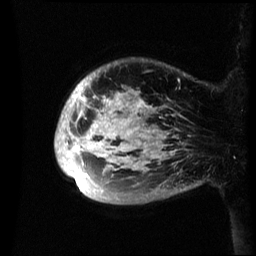
Breast MRI (dynamic contrast-enhanced), one sagittal slice. Slice 7 of 60 in the series (ordered by position). Dynamic contrast-enhanced series, image 2 of 3 at this slice position (ordered by acquisition). 1.5 T. TE 4.2 ms, TR 8.4 ms. 2.4 mm slice thickness. 256 × 256 image matrix. Female patient, age 48 years.
Structures marked on this image (semi-automatic segmentation, software-assisted and operator-edited):
- analysis volume of interest (the breast-tissue region the enhancement analysis was run in; not a lesion): bounding box (x1, y1, x2, y2) in pixels: (55, 65, 192, 204)
- tumour enhancement mask (voxels above the 70 % enhancement threshold inside the analysis volume of interest): (55, 80, 176, 186)